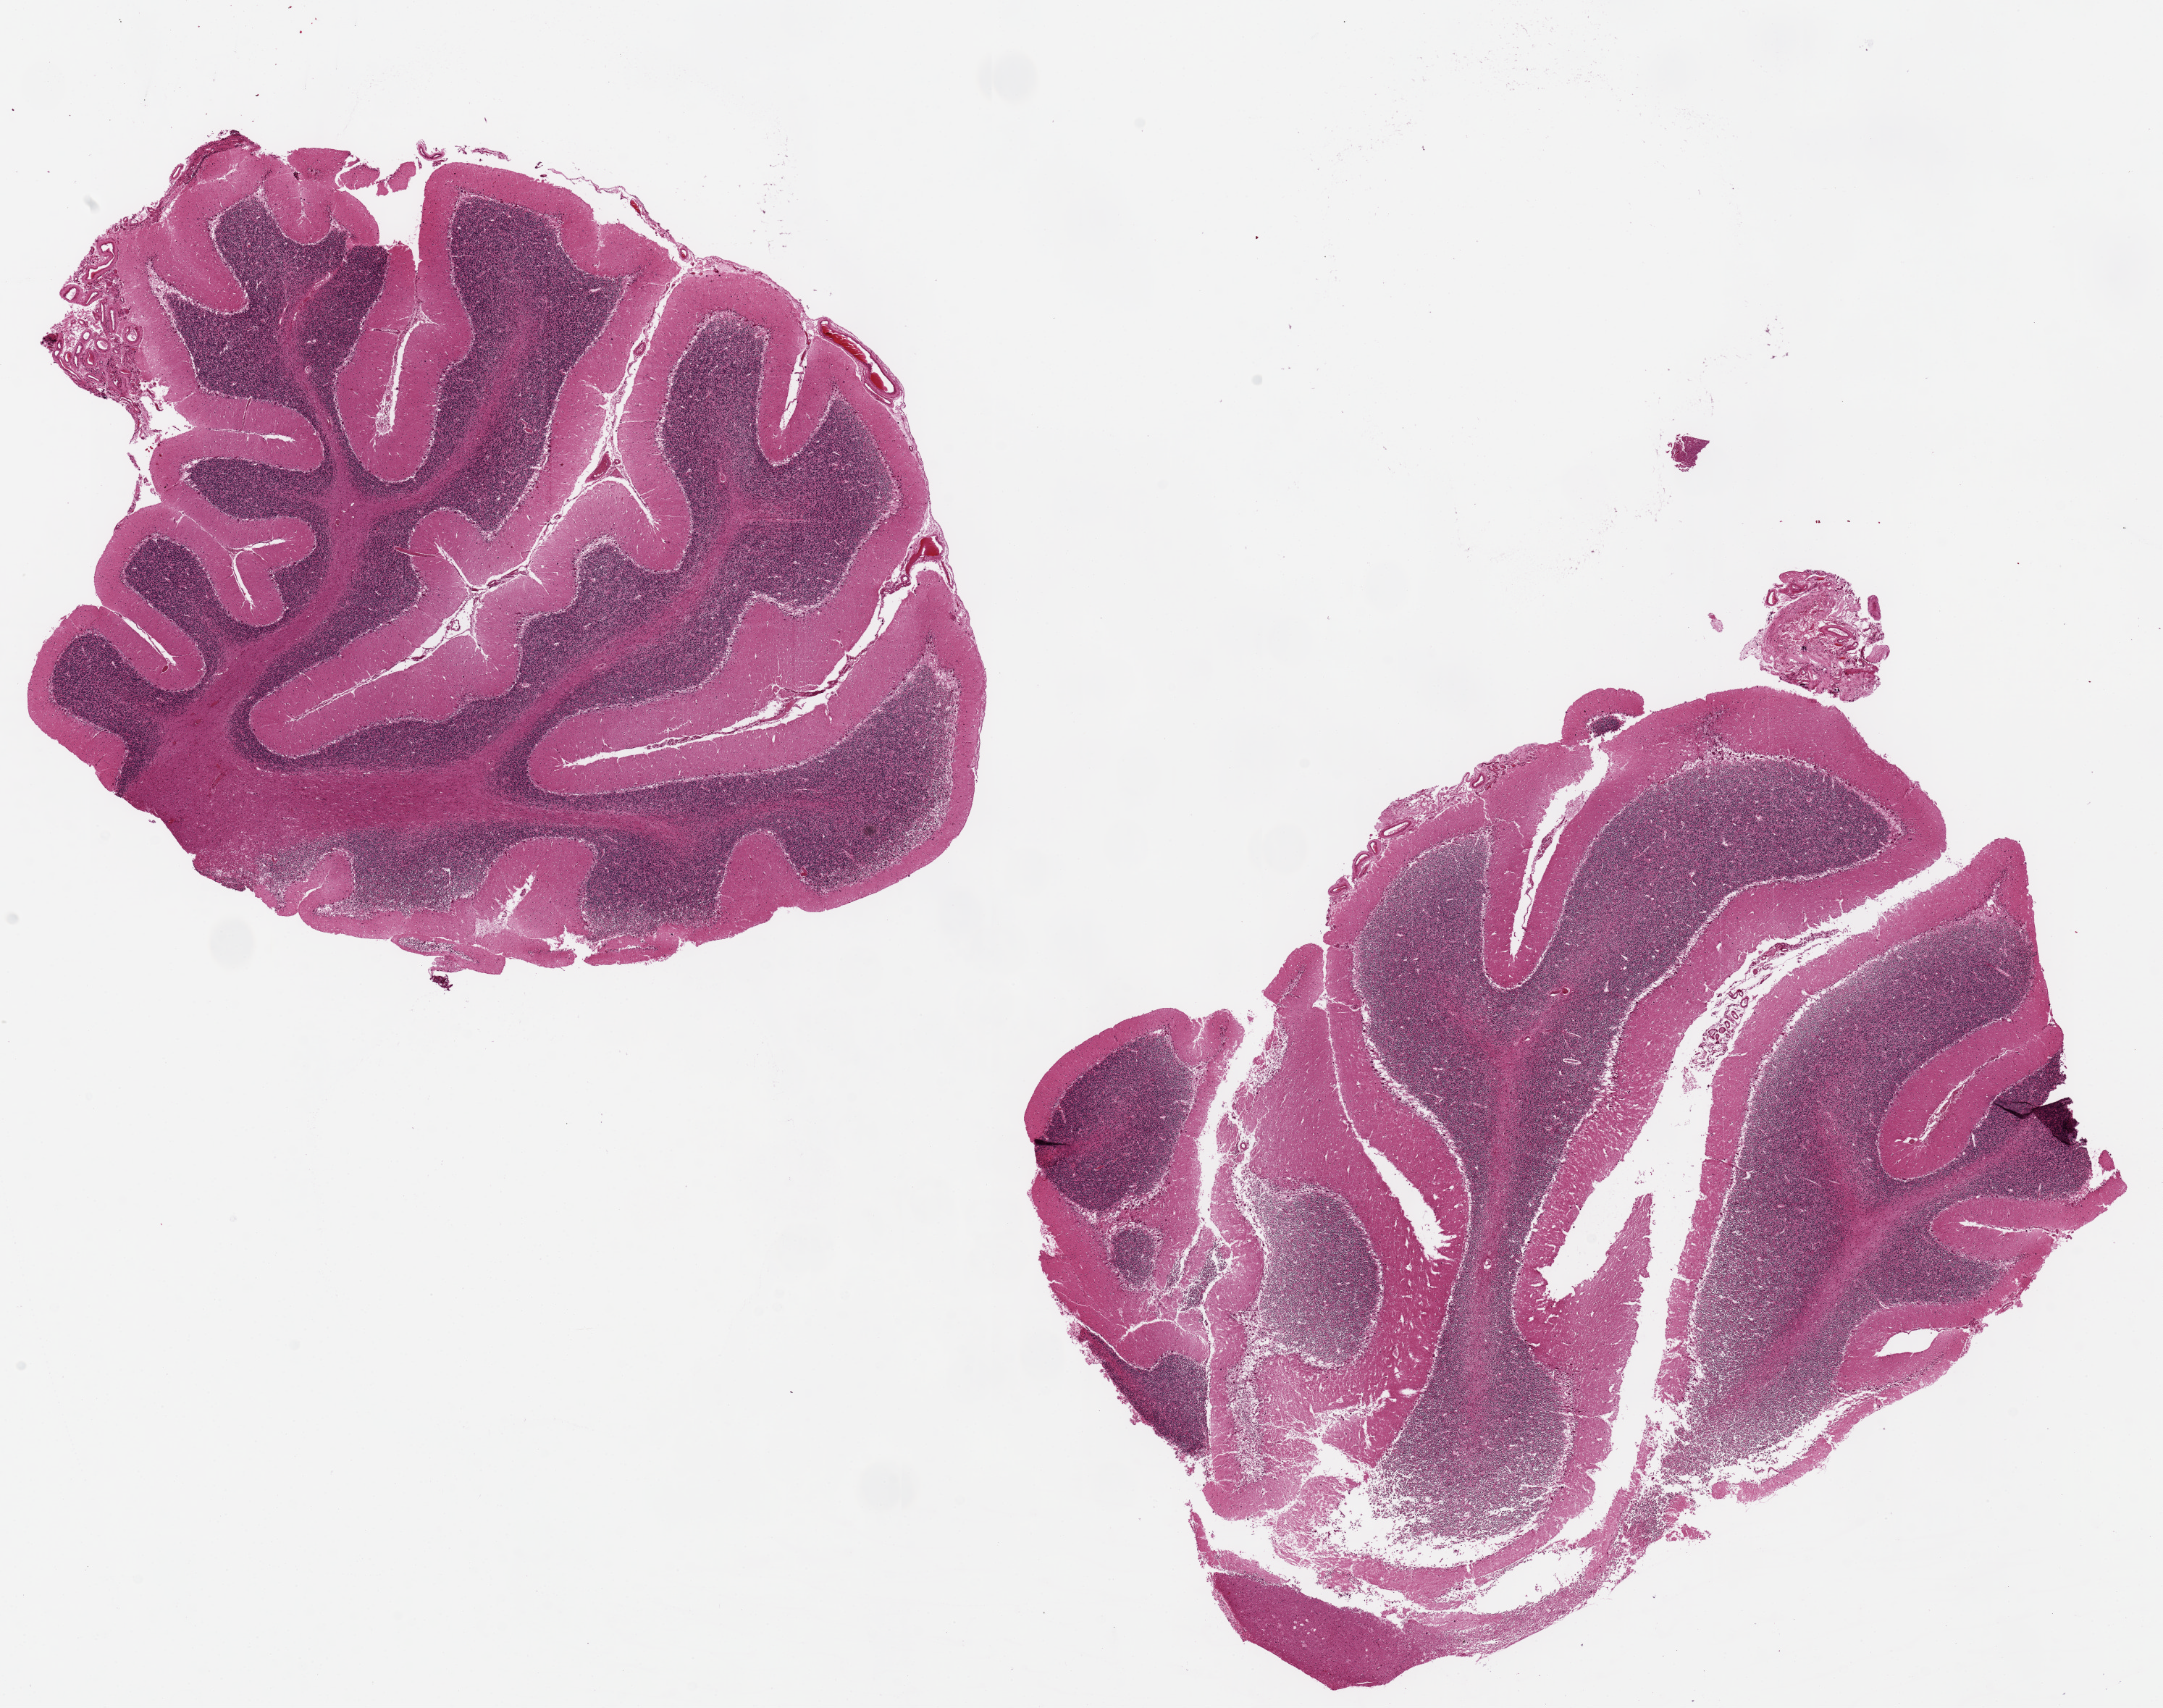
Whole-slide image, hematoxylin and eosin (H&E) stain — low-resolution overview of the scanned area, about 23.6 x 18.7 mm (from a 20x scan). PAXgene-fixed, paraffin-embedded tissue. Target tissue: cerebellum. Donor tissue sample.
Reviewer comment on this tissue sample: OK for analysis.